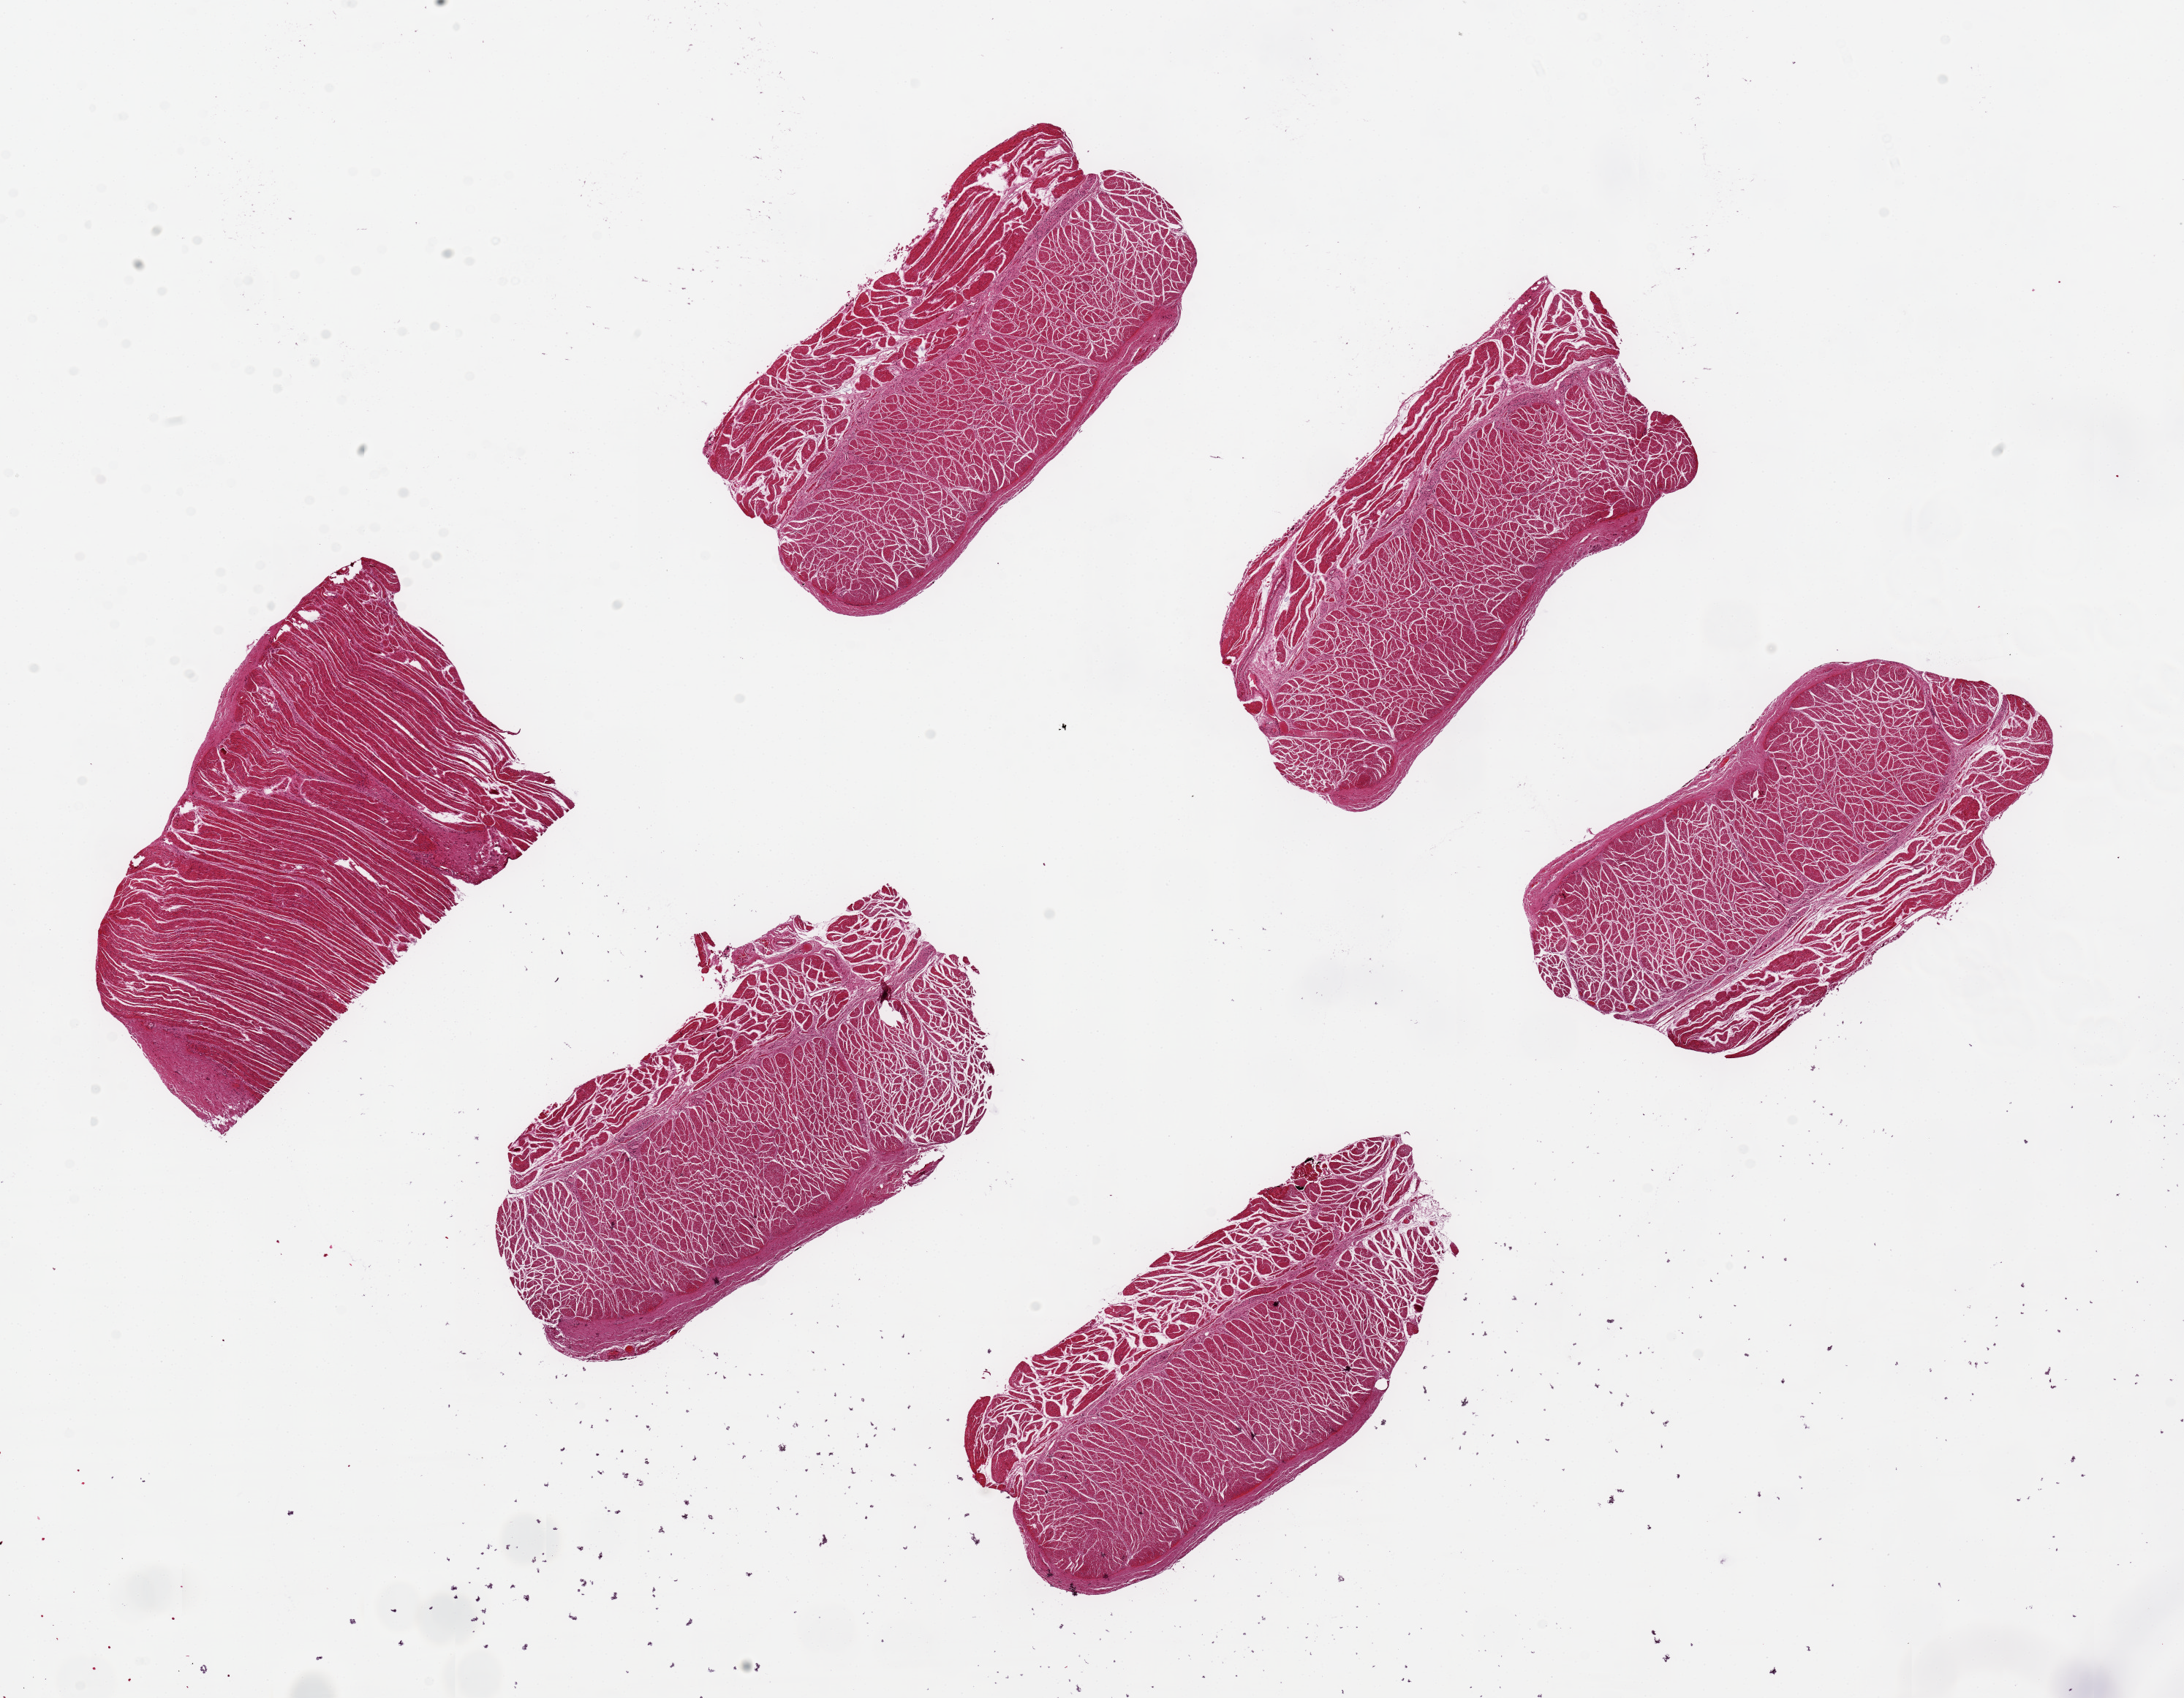
Digitized H&E-stained section — whole scanned area (about 23.6 x 18.4 mm) shown as a low-resolution overview, PAXgene-fixed paraffin-embedded (PFPE) section, section of esophageal muscle (target tissue), donor tissue sample. Male donor.
Pathologist's review note for this sample: 6 pieces ~7x3mm.